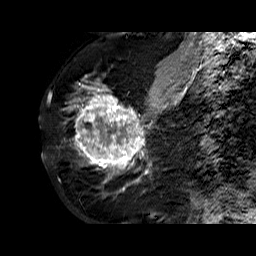
Breast MRI (dynamic contrast-enhanced), one sagittal slice. Position 28 of 60 along the scan axis. Dynamic contrast-enhanced series, time point 2 of 6 at this slice position (early post-contrast). 1.5 T. TE 6.3 ms, TR 32.4 ms. 4 mm slice thickness. 256 × 256 image matrix. Female patient. From the clinical record (not read from this slice): setting: breast cancer imaged before/during neoadjuvant chemotherapy; receptor status: HR-positive, HER2-negative.
Outlined on this slice (semi-automatically segmented with operator editing):
- analysis volume of interest (the breast-tissue region the enhancement analysis was run in; not a lesion): bounding box (x1, y1, x2, y2) in pixels: (68, 72, 177, 183)
- tumour enhancement mask (voxels above the 100 % enhancement threshold inside the analysis volume of interest): (68, 83, 168, 183)